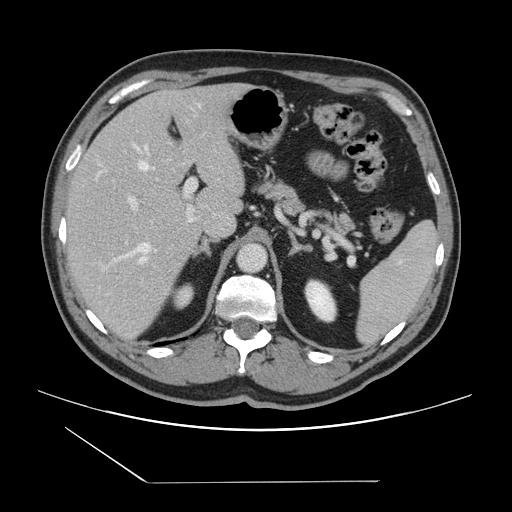
Contrast-enhanced abdominal CT, one axial slice; position 93 of 157 along the scan axis; 120 kVp; intravenous contrast given; soft-tissue window (W 400 / L 40 HU); 2.5 mm slice thickness; 512 × 512 image matrix, field of view 407 × 407 mm. Male patient, age 61 years. Case-level facts recorded for this patient, not image findings: diagnosis: colorectal cancer liver metastases, imaged before liver resection; multiple liver metastases: yes; largest metastasis: 5.5 cm; disease in both lobes: yes.
Annotated regions visible in this slice (expert manual segmentation):
- hepatic veins: box from (x=103, y=144) to (x=152, y=268) px
- liver: (x=65, y=85)–(x=245, y=339)
- planned liver remnant (the part of the liver to remain after resection): (x=67, y=85)–(x=237, y=223)
- portal vein (with intrahepatic branches): (x=128, y=178)–(x=197, y=222)